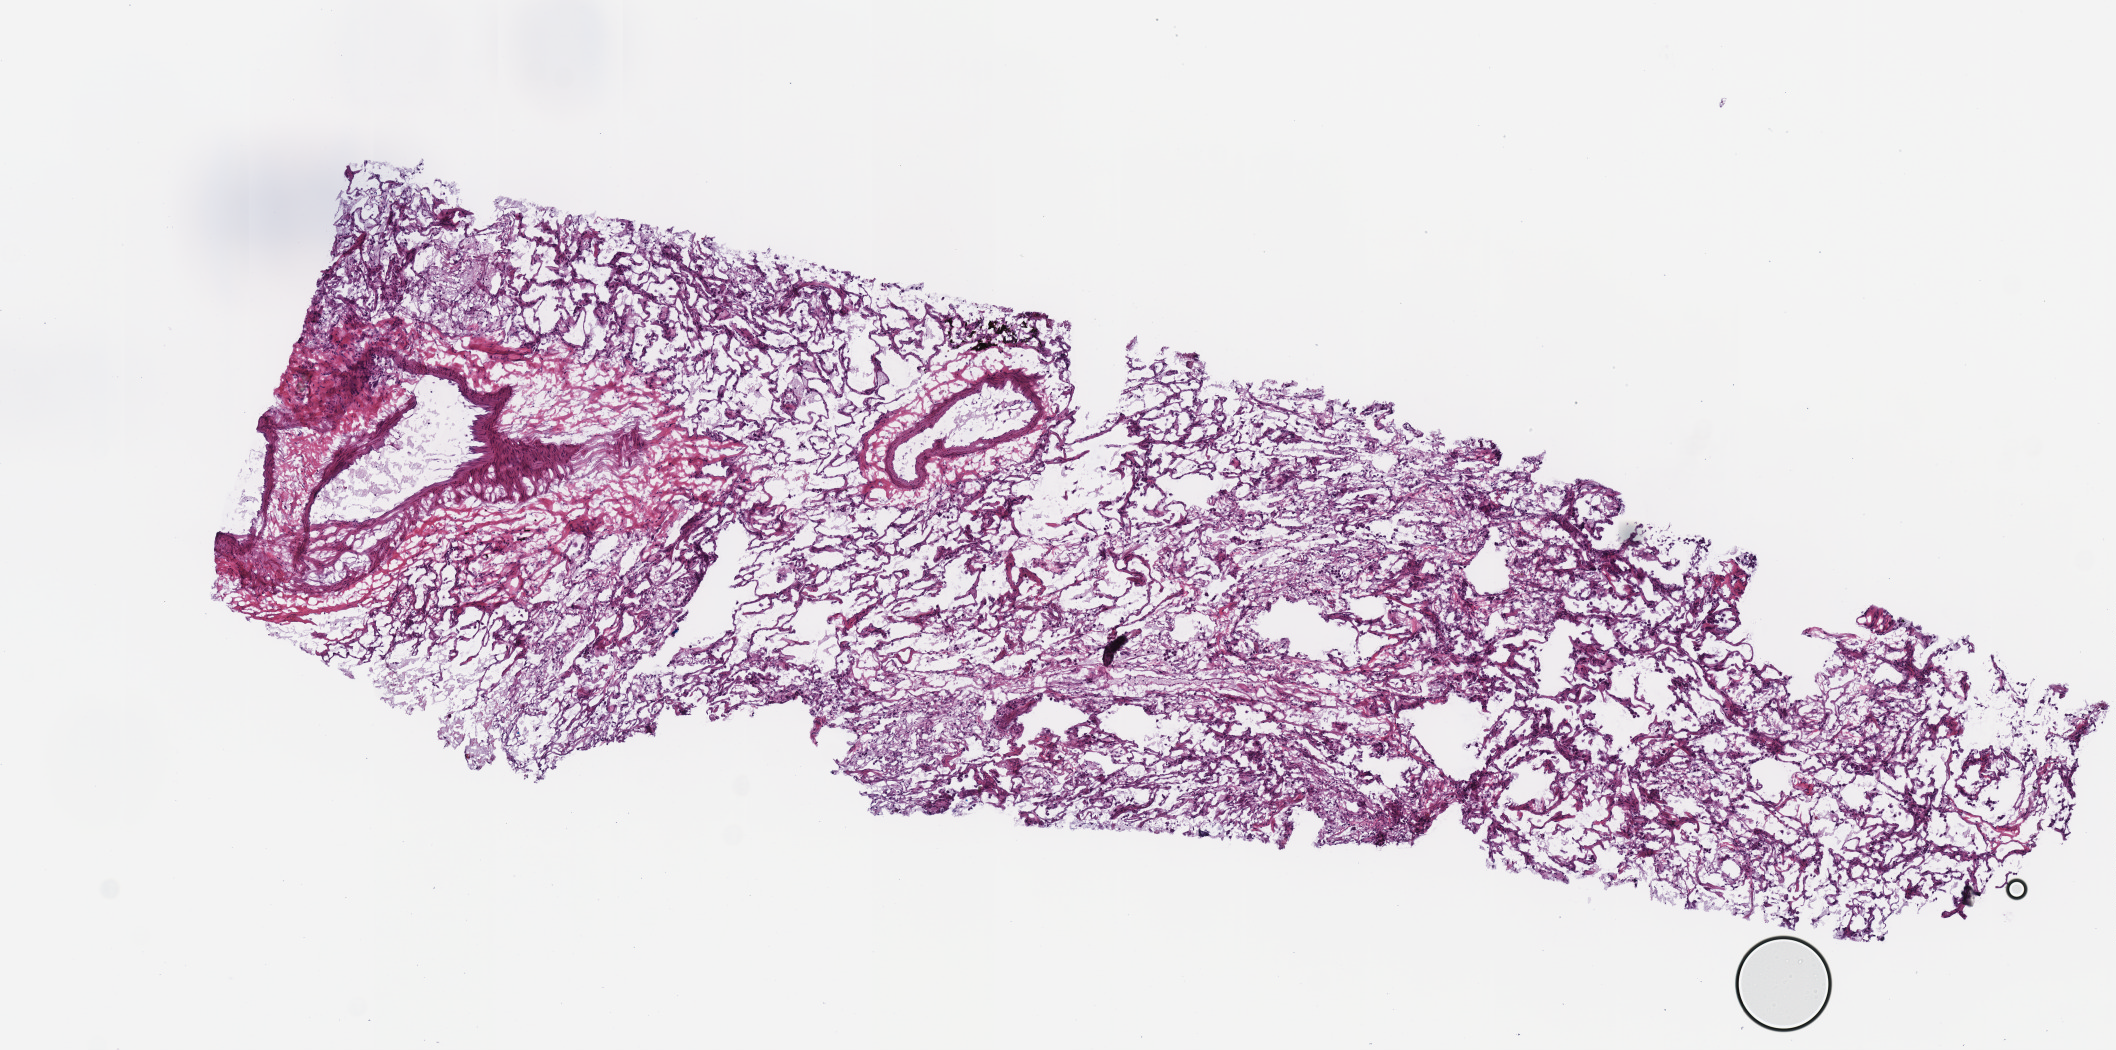
Whole-slide histology image, H&E-stained — low-resolution overview of the scanned area, about 8.3 x 4.1 mm (acquisition: 40x scan). Frozen section from the top of the tissue portion. Solid tissue normal (non-tumour tissue) sample from the lung. Male, age 68 years at initial diagnosis.
• this section: solid tissue normal (non-tumour) sample from the same patient
• patient diagnosis: Squamous cell carcinoma, NOS